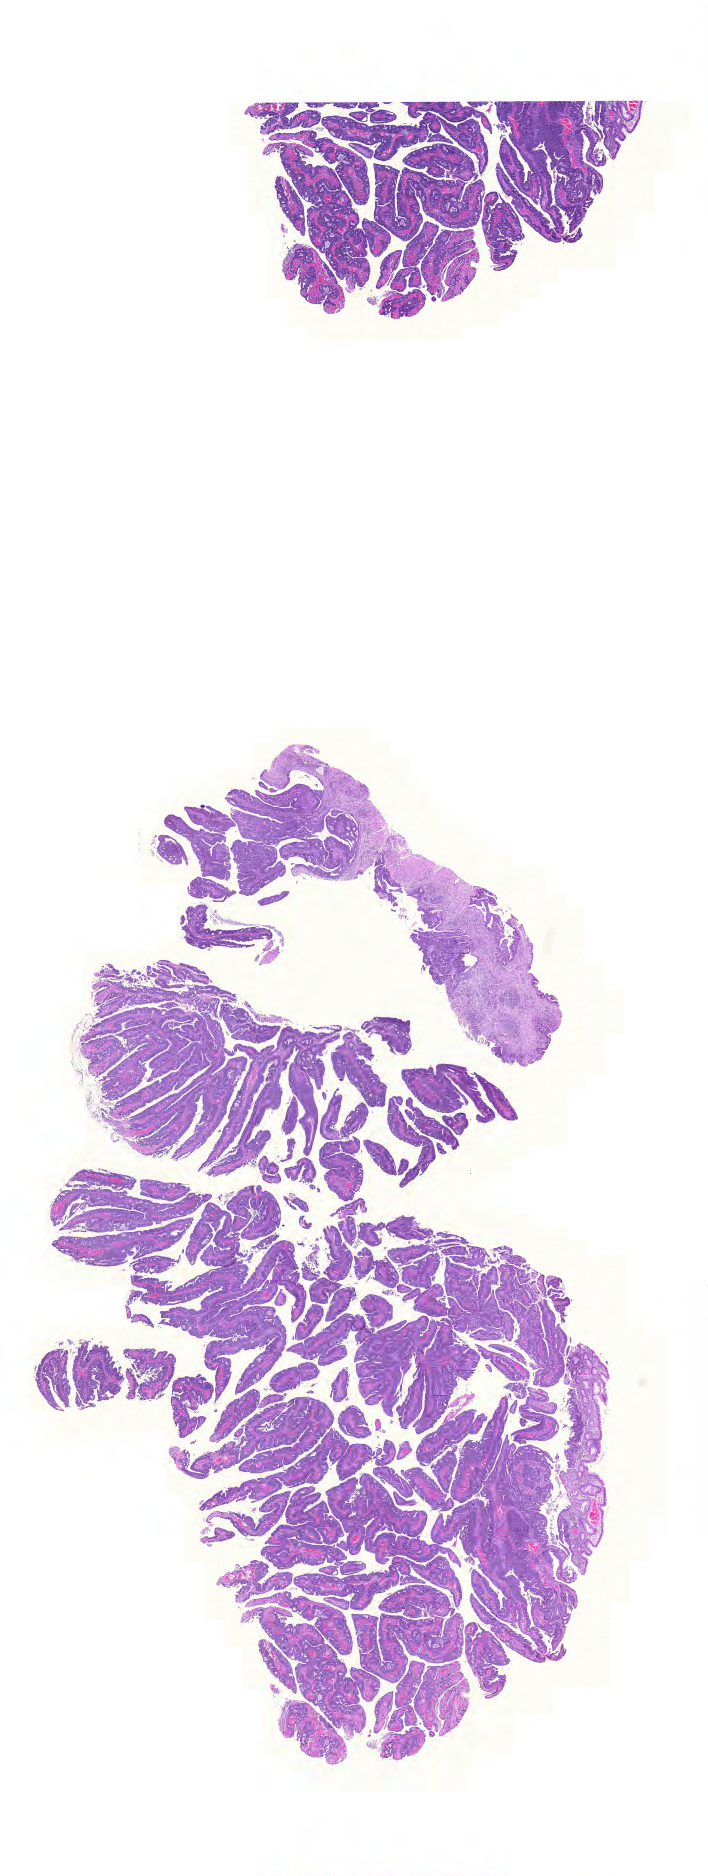
Digitized Hematoxylin and eosin (H&E) stained tissue section (whole slide) — a low-resolution overview of the entire scanned area, about 10.5 x 27.9 mm (slide scanned at 20x). Formalin-fixed paraffin-embedded (FFPE) diagnostic section. Primary tumour sample from the rectum. Patient: male, age at initial diagnosis 69 years.
- pathologic diagnosis: Adenocarcinoma, NOS (rectosigmoid junction)
- AJCC pathologic stage: IIA (6th edition)
- lymph nodes positive (case pathology): 0 of 65 examined